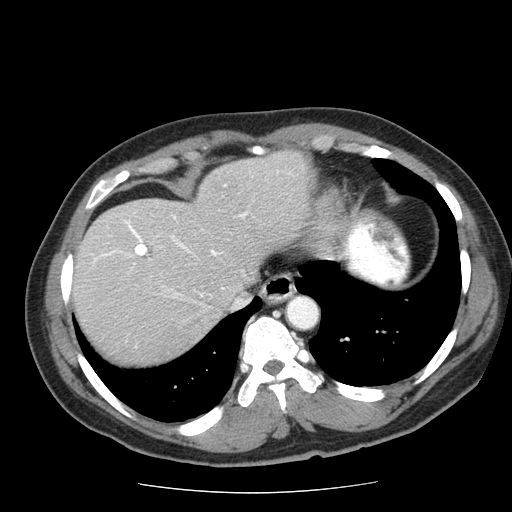
Contrast-enhanced abdominal CT (liver protocol), one axial slice. Position 55 of 85 along the scan axis. Reconstruction kernel STANDARD. Soft-tissue window (W 400 / L 40 HU). 2.5 mm slice thickness. 512 × 512 image matrix, field of view 360 × 360 mm. From the clinical record (not read from this slice): diagnosis: hepatocellular carcinoma (patient treated with transarterial chemoembolisation; whether this scan precedes or follows treatment is not stated here); TNM stage (as recorded): Stage-IIIA; Child-Pugh class: A; tumour differentiation: well differentiated; tumour nodularity: multinodular.
Outlined on this slice (semi-automatically segmented with operator editing):
- liver parenchyma outside the tumour (the mass and vessels are separate outlines, so this box may not span the whole liver): bounding box (x1, y1, x2, y2) in pixels: (72, 150, 310, 364)
- liver vessels: (93, 171, 290, 296)